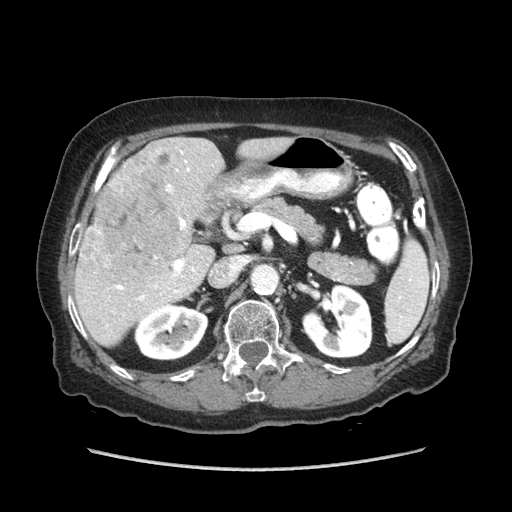
Contrast-enhanced abdominal CT (liver protocol), one axial slice; position 39 of 89 along the scan axis; 140 kVp; soft-tissue window (W 400 / L 40 HU); 2.5 mm slice thickness; 512 × 512 image matrix. Case-level facts recorded for this patient, not image findings: diagnosis: hepatocellular carcinoma (patient treated with transarterial chemoembolisation; whether this scan precedes or follows treatment is not stated here); TNM stage (as recorded): Stage-IIIA; Child-Pugh class: A; tumour size: 11 cm.
Structures marked on this image (semi-automatically segmented with operator editing):
- liver parenchyma outside the tumour (the mass and vessels are separate outlines, so this box may not span the whole liver): box from (x=74, y=138) to (x=291, y=346) px
- mass: (x=92, y=142)–(x=182, y=279)
- liver vessels: (x=97, y=151)–(x=195, y=301)